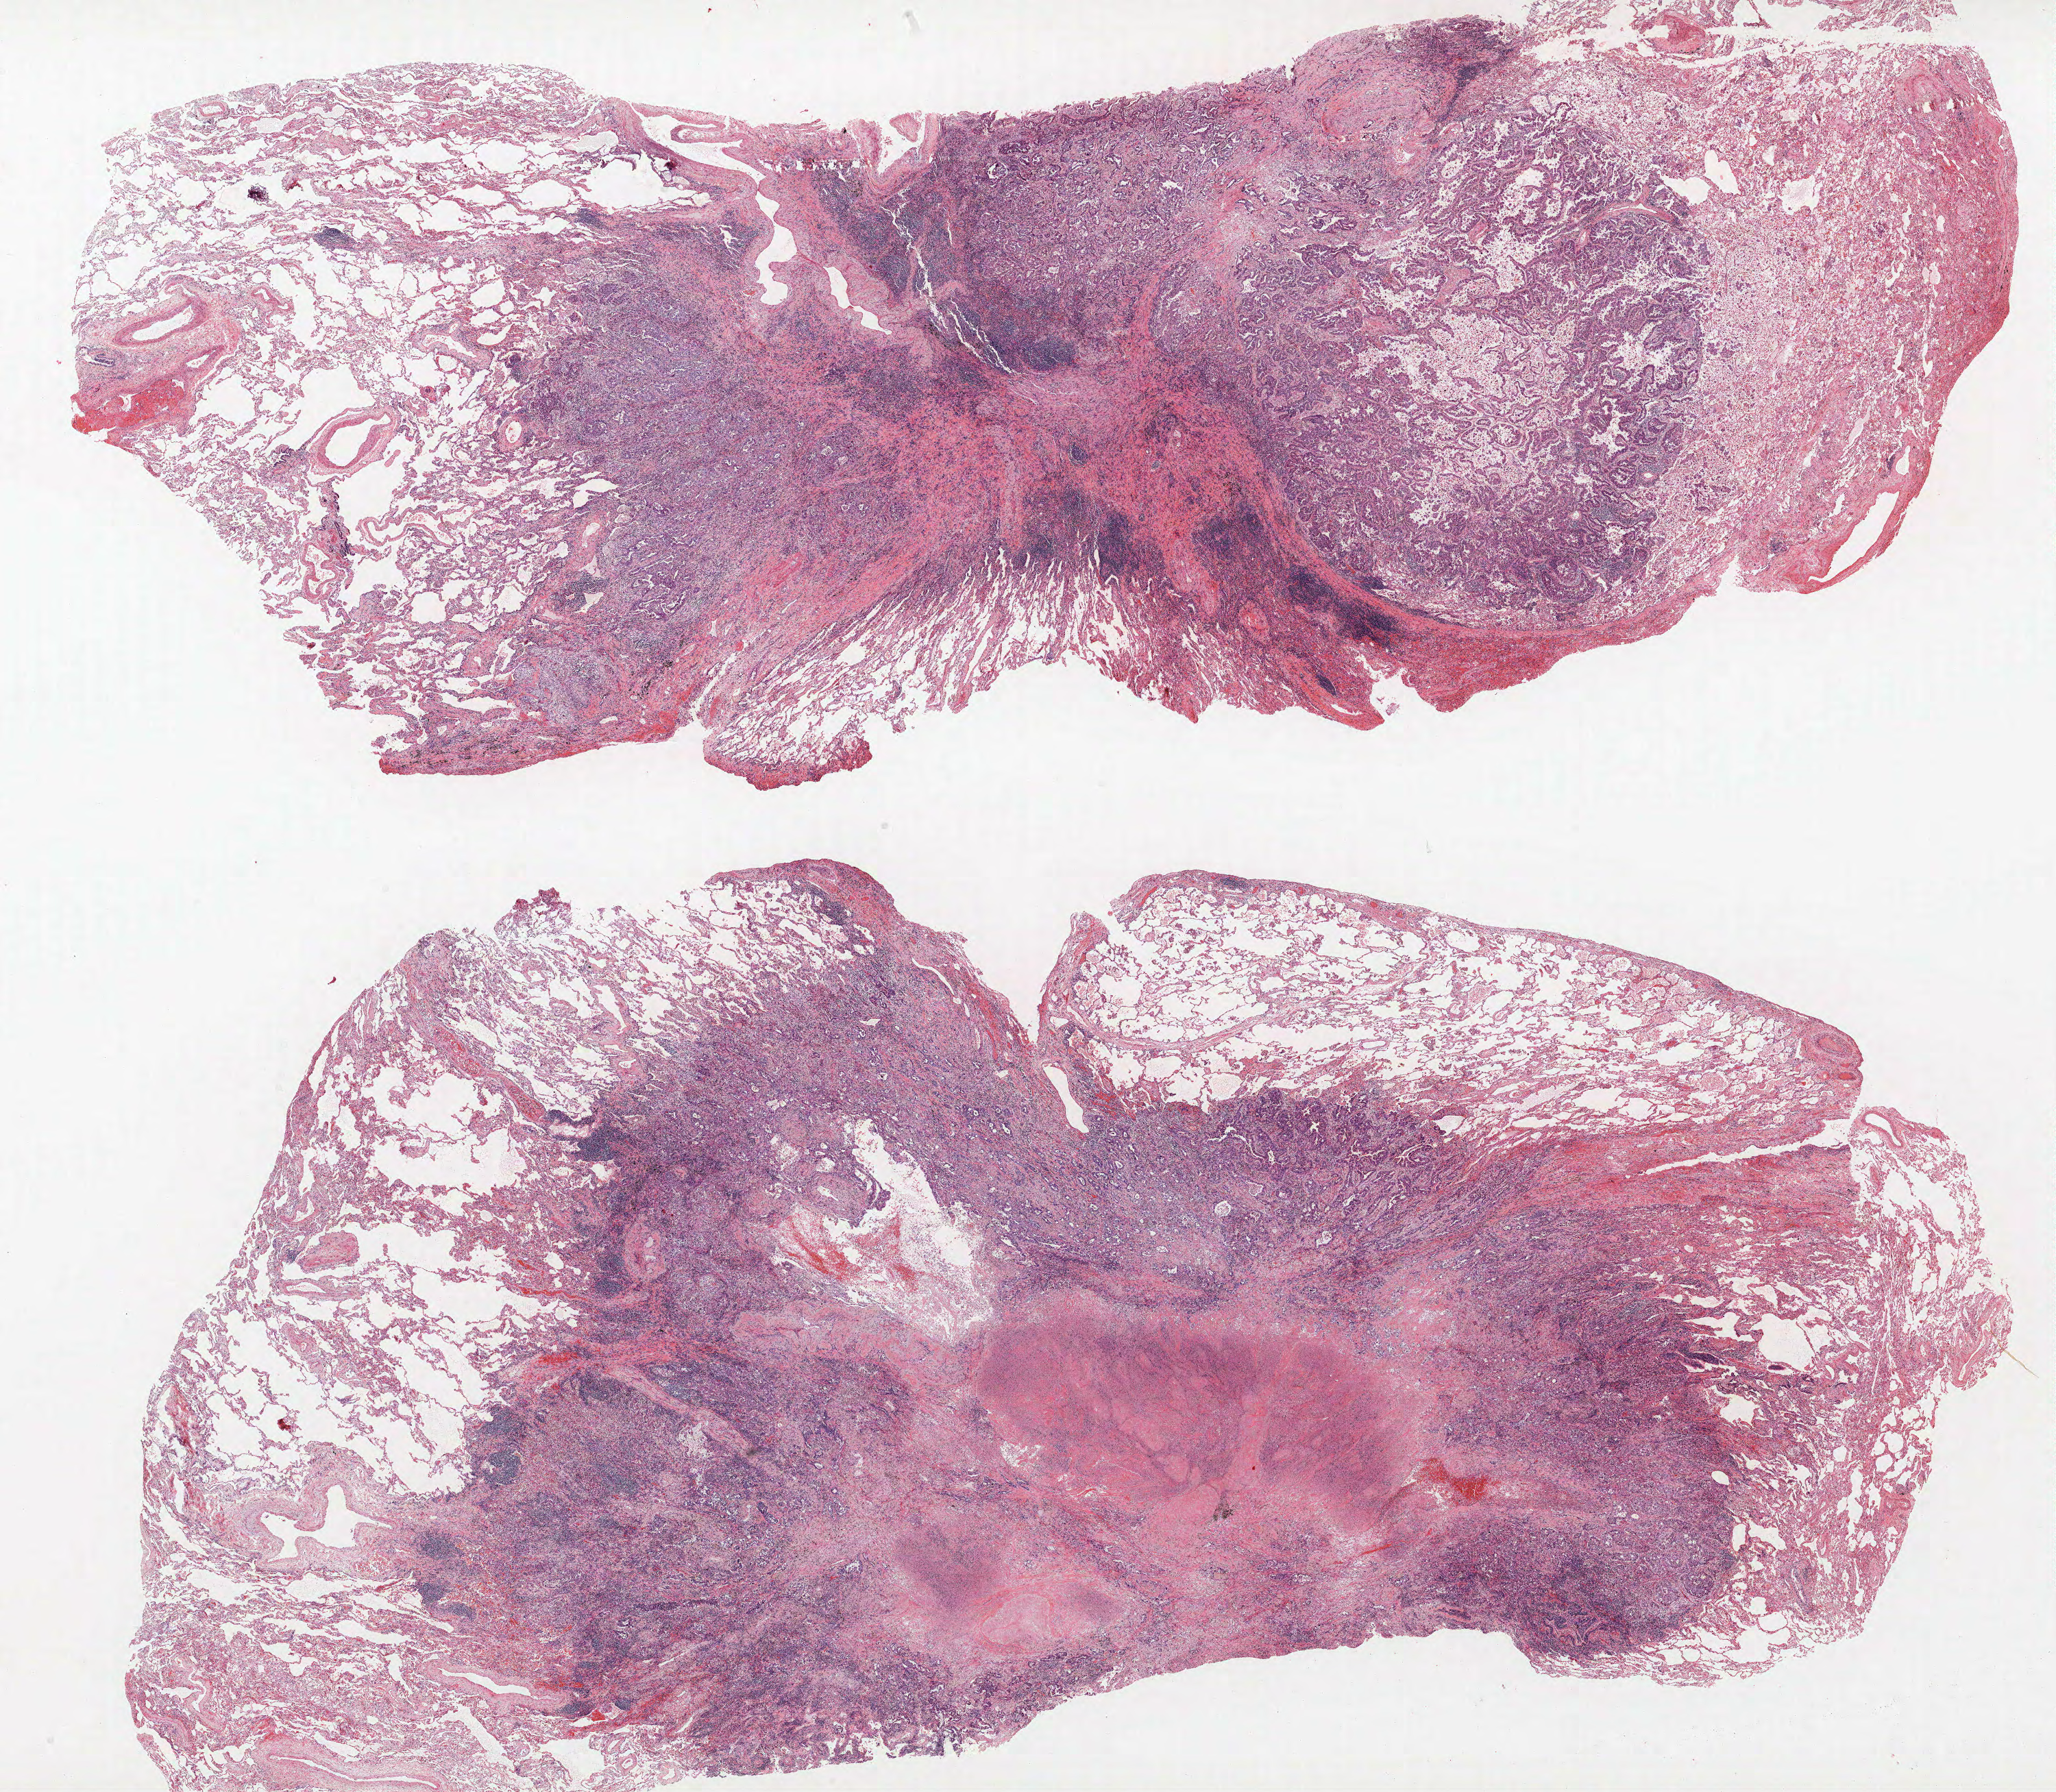
Hematoxylin and eosin (H&E) stained whole-slide image, shown as a low-resolution overview of the whole scanned area (about 24.0 x 20.9 mm, from a 40x scan). Formalin-fixed paraffin-embedded (FFPE) section. Lung tissue. Male patient, aged 69 at enrolment. Current smoker at enrolment. Grade: moderately differentiated (G2).
Tumour size (pathology): 20 mm. Participant's lung-cancer diagnosis: Adenocarcinoma, NOS (ICD-O-3 8140/3). Primary tumour location (clinical record): right upper lobe. Stage (AJCC 6th edition): IIA.